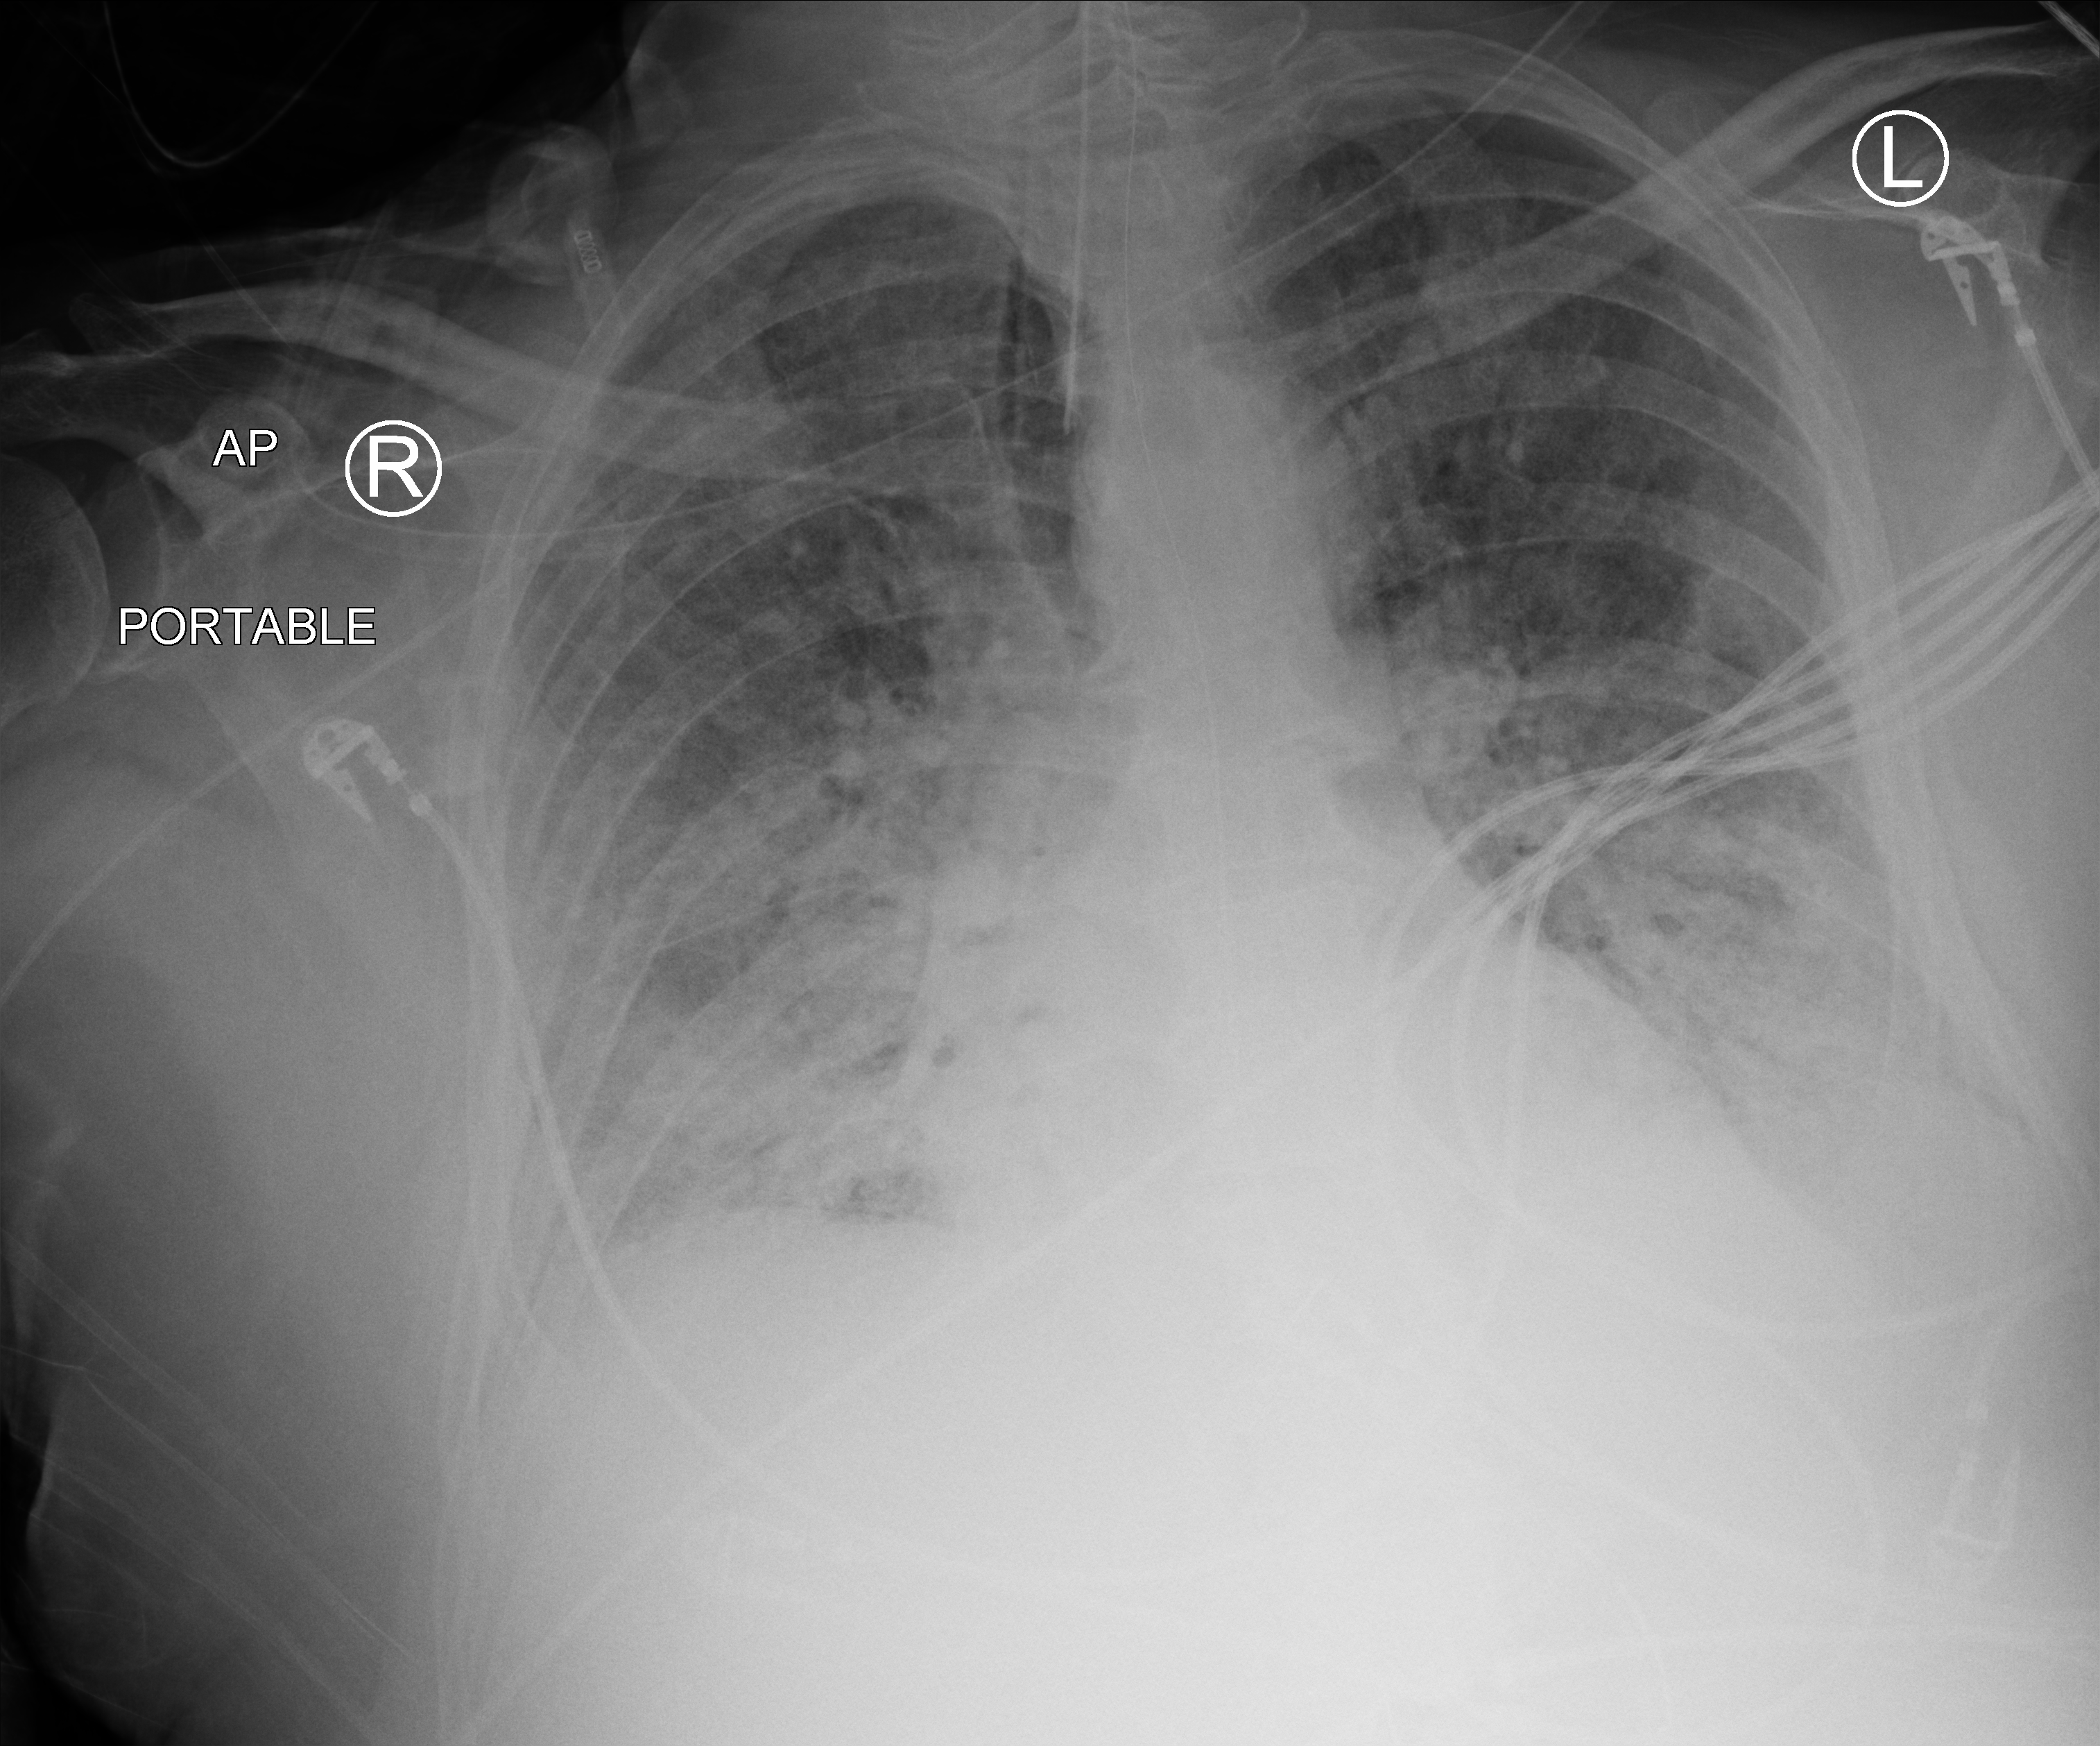
Bedside chest radiograph (computed radiography); anteroposterior (AP) projection. Male patient hospitalised with COVID-19, age 60–74 years.
From the hospital-stay record, not from the radiograph (when in the stay this image was taken is not recorded):
- other chronic lung disease (admission record): no